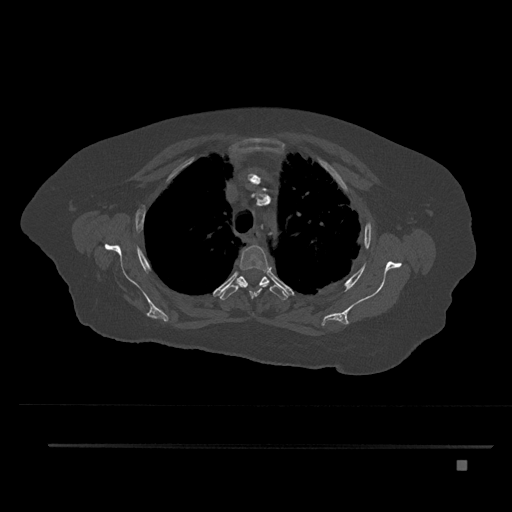
CT including the spine, one axial slice; bone window (W 1800 / L 400 HU); 0.5 mm slice thickness; 512 × 512 image matrix, field of view 437 × 437 mm. Patient: female, 76 years. Case-level facts recorded for this patient, not image findings: primary cancer: lung.
Outlined on this slice (semi-automatic segmentation, software-assisted and operator-edited):
- T3 vertebra: bounding box (x1, y1, x2, y2) in pixels: (235, 245, 270, 299)
- T4 vertebra: (219, 276, 289, 300)